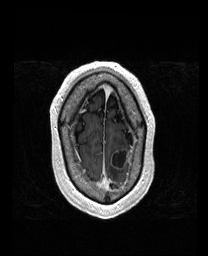
Brain MRI from a brain-tumour surgery series, one axial slice. Slice 153 of 192 in the series (ordered by position). T1-weighted post-contrast. 1 mm slice thickness. 208 × 256 image matrix, field of view 211 × 260 mm. Case-level facts recorded for this patient, not image findings: histopathology: Metastatic Carcinoma from Lung Adenocarcinoma; tumour location: Left Frontal.
Structures marked on this image (expert manual segmentation):
- tumour: box from (x=113, y=149) to (x=129, y=168) px